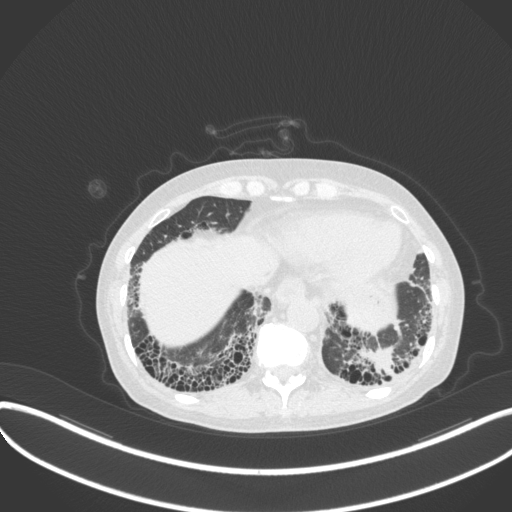
Chest CT, one axial slice. Slice 63 of 373 in the series (ordered by position). 120 kVp. Lung window (W 1500 / L -600 HU). 1 mm slice thickness. 512 × 512 image matrix. Patient: female, 56 years. From the clinical record (not read from this slice): clinical TNM (as recorded): T1 N0 M0.
Outlined on this slice (bounding box drawn by a radiologist):
- lung tumour (recorded histology: adenocarcinoma): box from (x=358, y=347) to (x=398, y=381) px